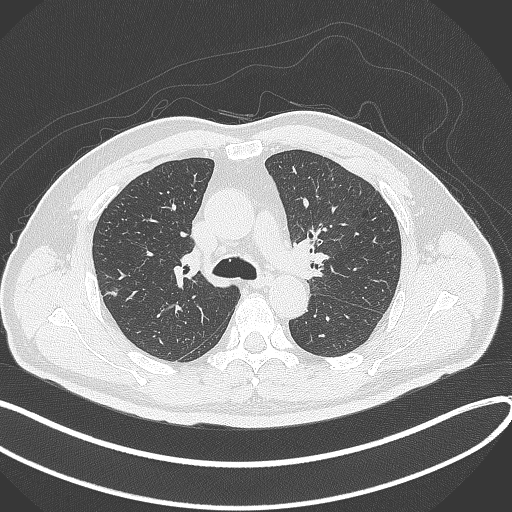
Chest CT, one axial slice. Position 226 of 372 along the scan axis. Lung window (W 1500 / L -600 HU). 1 mm slice thickness. 512 × 512 image matrix. Male patient, age 60 years. Case-level facts recorded for this patient, not image findings: clinical TNM (as recorded): T1c N0 M0.
Structures marked on this image (bounding box drawn by a radiologist):
- lung tumour (recorded histology: adenocarcinoma): bounding box [x1, y1, x2, y2] px = [99, 282, 124, 302]